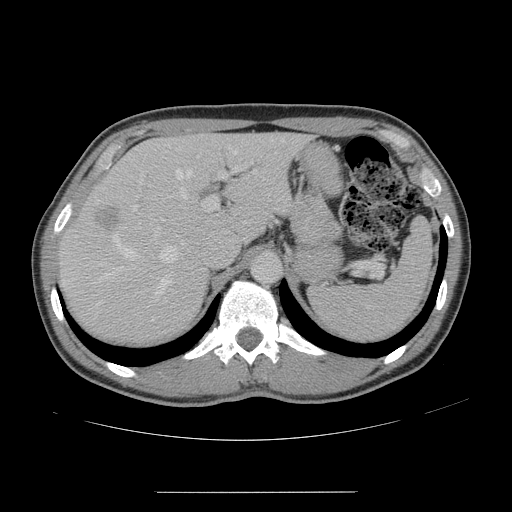
Contrast-enhanced abdominal CT, one axial slice. Slice 106 of 178 in the series (ordered by position). 120 kVp. Intravenous contrast given. Soft-tissue window (W 400 / L 40 HU). 2.5 mm slice thickness. 512 × 512 image matrix, field of view 401 × 401 mm. Male patient, age 53 years. From the clinical record (not read from this slice): diagnosis: colorectal cancer liver metastases, imaged before liver resection; multiple liver metastases: yes; largest metastasis: 2.4 cm; disease in both lobes: no.
Structures marked on this image (manually delineated by an expert):
- hepatic veins: bounding box (x1, y1, x2, y2) in pixels: (104, 139, 284, 306)
- liver: (62, 134, 304, 341)
- planned liver remnant (the part of the liver to remain after resection): (148, 135, 304, 239)
- portal vein (with intrahepatic branches): (133, 156, 253, 236)
- liver metastasis: (96, 204, 123, 232)